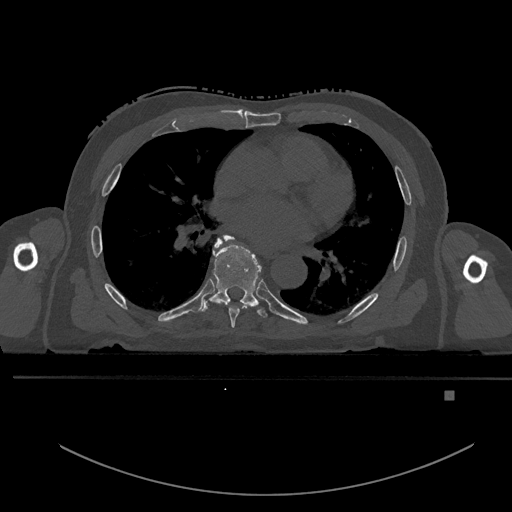
CT including the spine, one axial slice. Position 275 of 969 along the scan axis. Bone window (W 1800 / L 400 HU). 0.5 mm slice thickness. 512 × 512 image matrix. Male patient, age 82 years. Case-level facts recorded for this patient, not image findings: primary cancer: prostate.
Annotated regions visible in this slice (semi-automatic segmentation, software-assisted and operator-edited):
- T6 vertebra: box from (x=214, y=238) to (x=249, y=328) px
- T7 vertebra: (x=202, y=235)–(x=267, y=318)